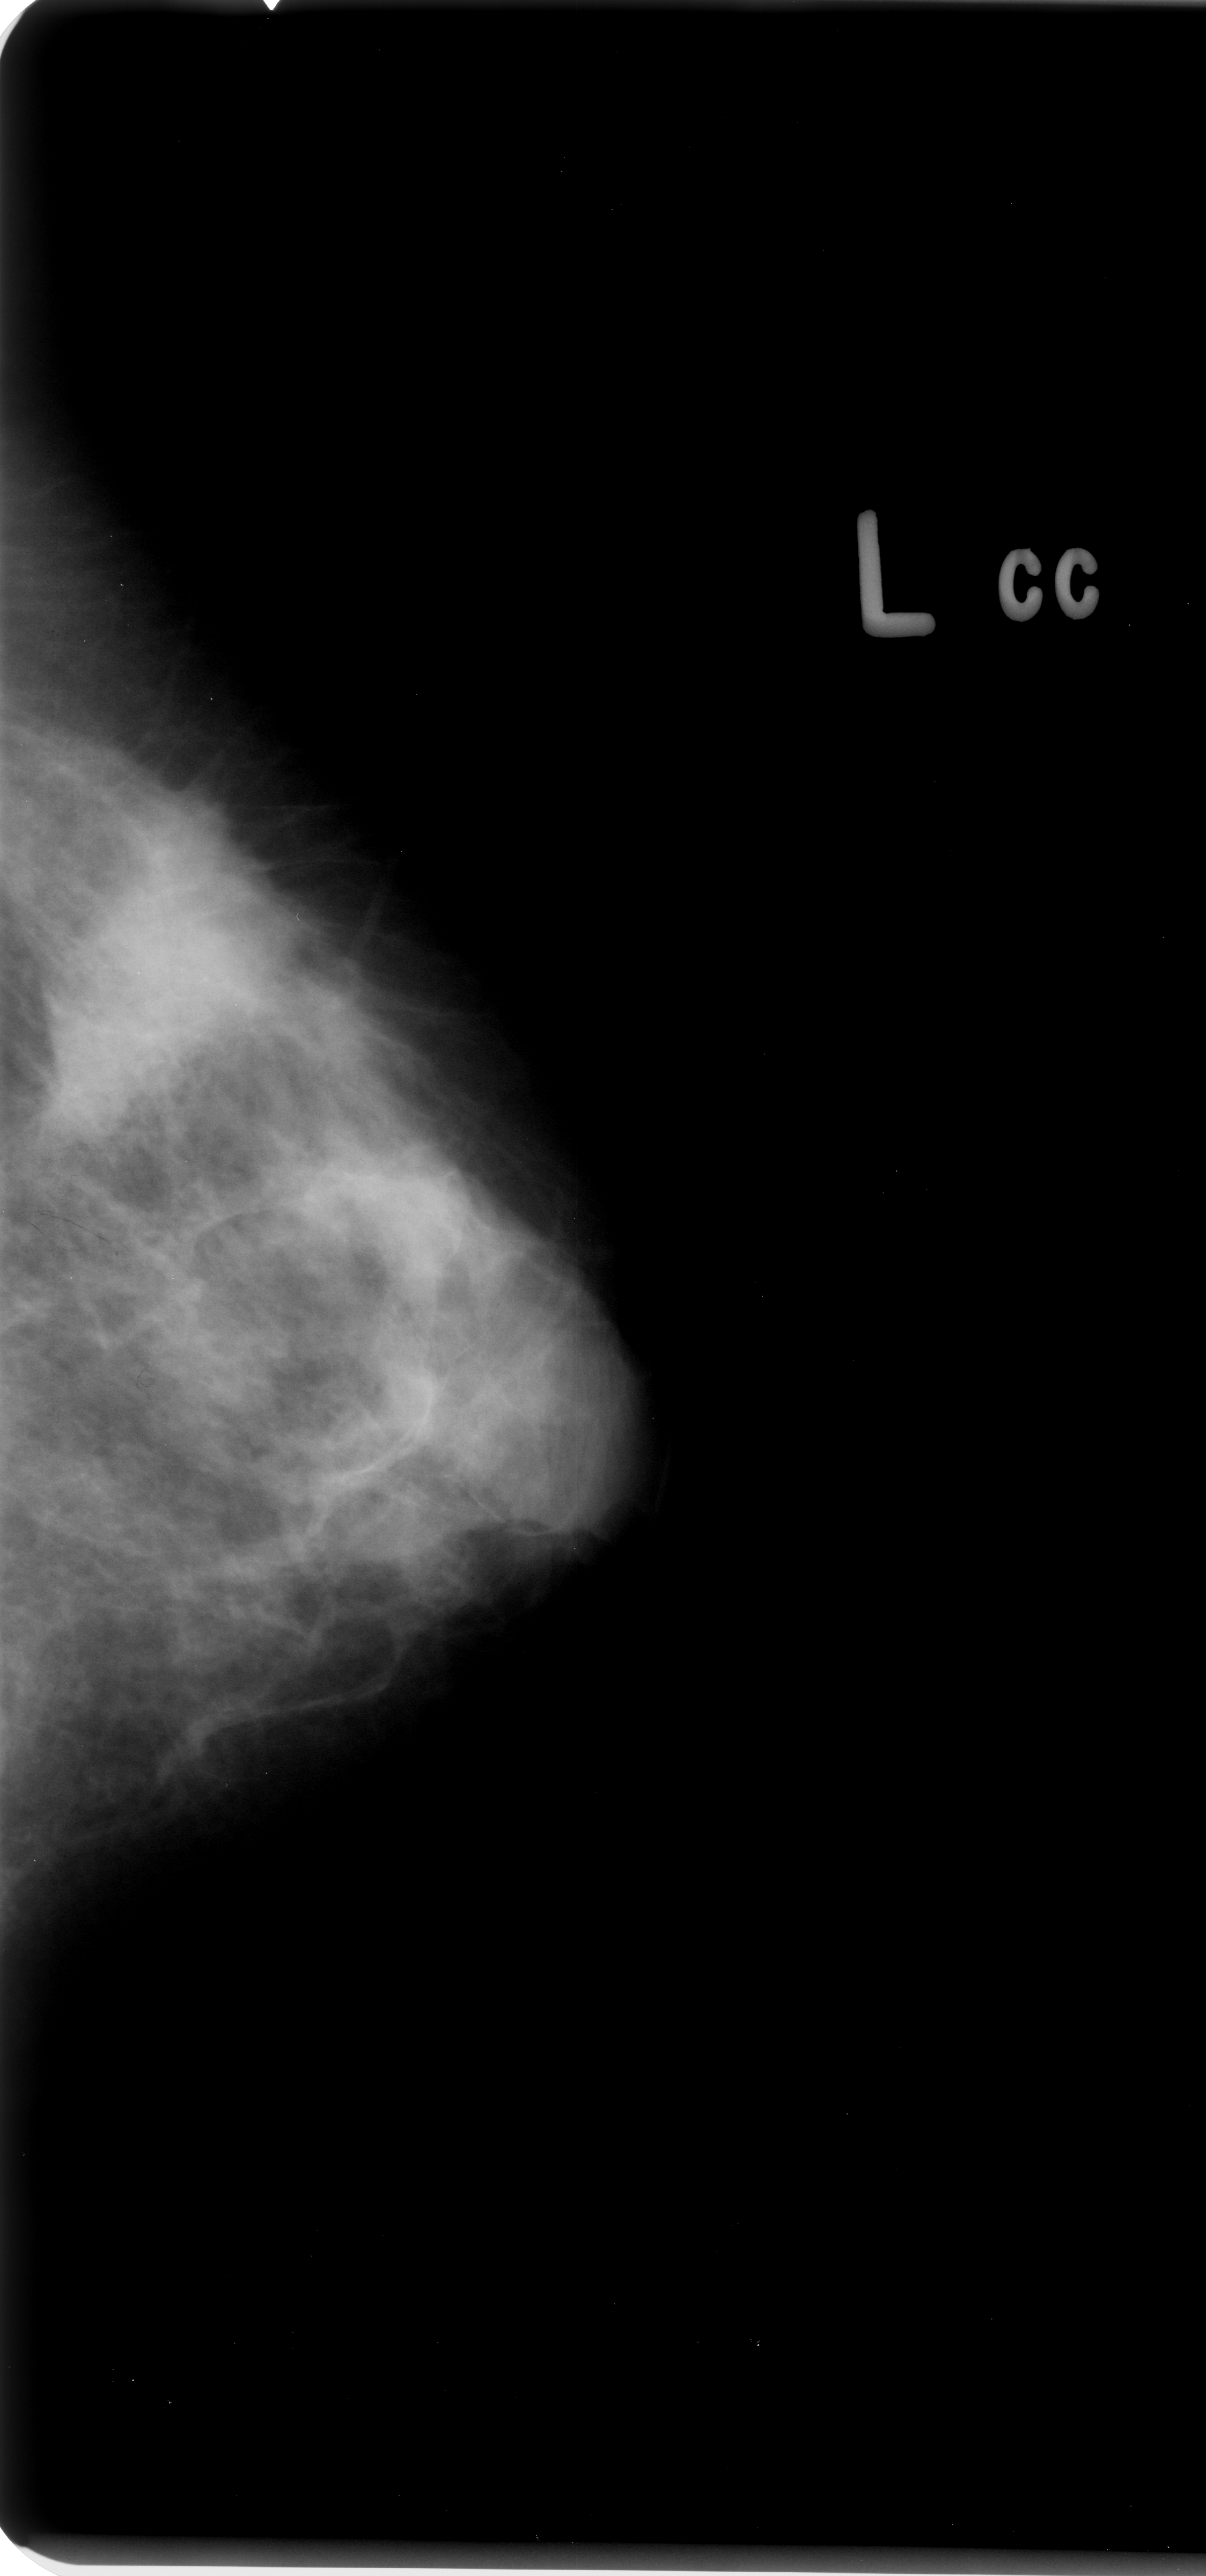
Digitized screen-film mammogram; left breast; craniocaudal (CC) view; BI-RADS breast density category 3 (scale 1–4); 1206 × 2576 image matrix.
Expert-marked regions of interest on this image (one box per marked abnormality):
- mass, shape irregular / architectural distortion, margins obscured / spiculated; BI-RADS assessment category 4; subtlety rating 4 on a 1 (subtle) to 5 (obvious) scale; pathology (as recorded): malignant: bounding box [x1, y1, x2, y2] px = [61, 808, 263, 1036]